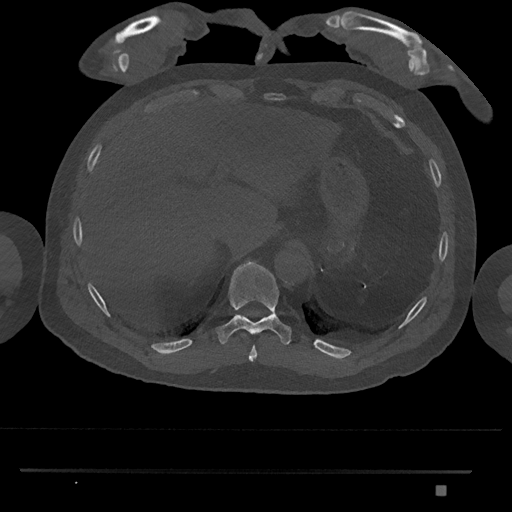
CT including the spine, one axial slice; position 1002 of 1134 along the scan axis; 120 kVp; bone window (W 1800 / L 400 HU); 0.5 mm slice thickness; 512 × 512 image matrix, field of view 429 × 429 mm. Male patient, age 65 years. From the clinical record (not read from this slice): primary cancer: prostate.
Outlined on this slice (semi-automatically segmented with operator editing):
- T10 vertebra: box from (x=216, y=261) to (x=292, y=345) px
- T9 vertebra: (x=248, y=345)–(x=257, y=362)